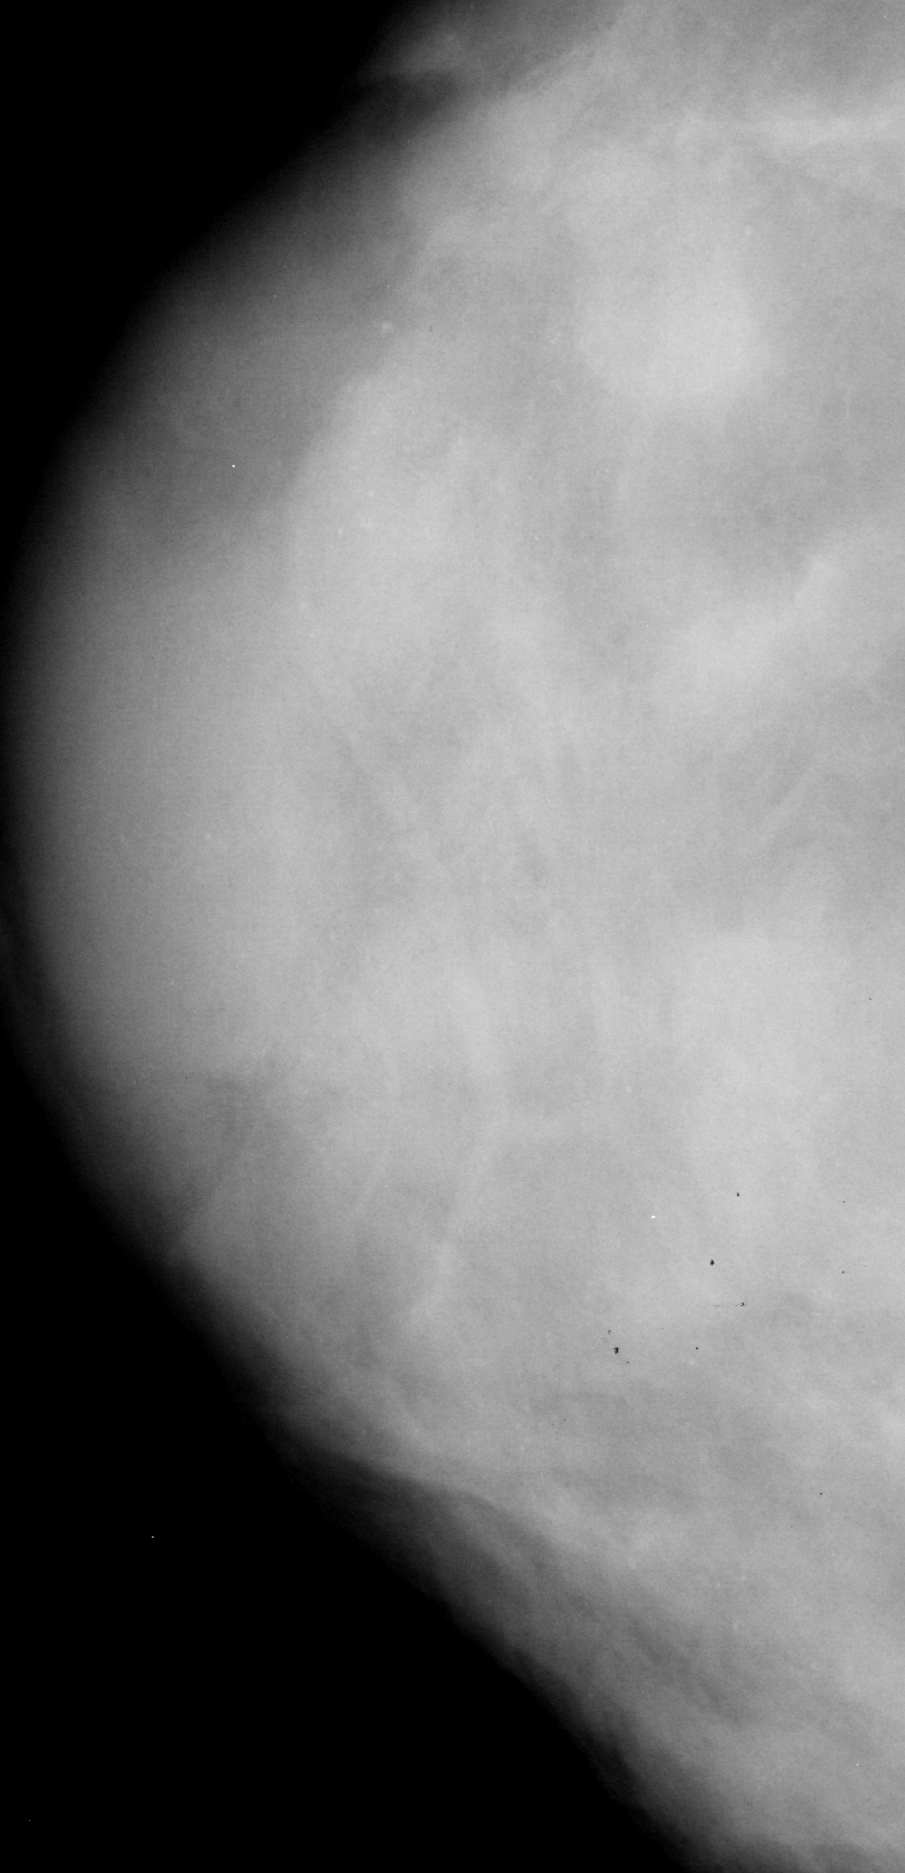
Cropped region of a digitized screen-film mammogram centred on a radiologist-marked abnormality, right breast, CC view.
Finding: calcifications, morphology pleomorphic, distribution regional; BI-RADS assessment category 4; pathology (as recorded): benign.